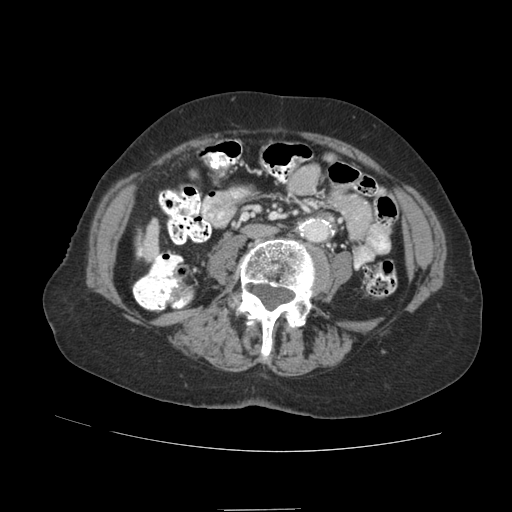
Contrast-enhanced abdominal CT (liver protocol), one axial slice. Slice 7 of 89 in the series (ordered by position). 140 kVp. Soft-tissue window (W 400 / L 40 HU). 512 × 512 image matrix, field of view 360 × 360 mm. From the clinical record (not read from this slice): diagnosis: hepatocellular carcinoma (patient treated with transarterial chemoembolisation; whether this scan precedes or follows treatment is not stated here); TNM stage (as recorded): Stage-II; Child-Pugh class: A; tumour differentiation: moderately differentiated; tumour nodularity: multinodular.
Outlined on this slice (semi-automatic segmentation, software-assisted and operator-edited):
- liver parenchyma outside the tumour (the mass and vessels are separate outlines, so this box may not span the whole liver): box from (x=138, y=218) to (x=158, y=258) px